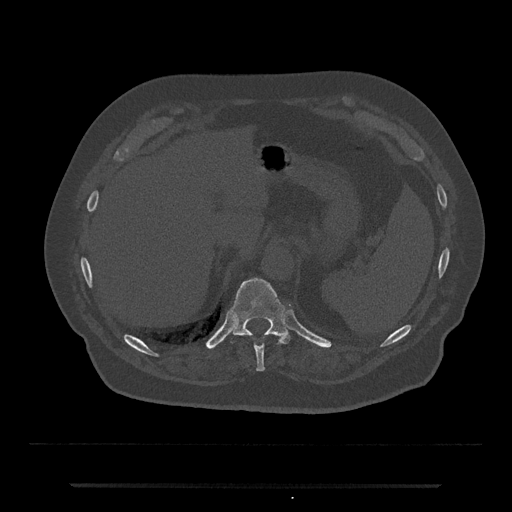
CT including the spine, one axial slice; slice 669 of 797 in the series (ordered by position); reconstruction kernel Br40s/3; 120 kVp; bone window (W 1800 / L 400 HU); 512 × 512 image matrix, field of view 434 × 434 mm. Patient: male, 80 years. Case-level facts recorded for this patient, not image findings: primary cancer: prostate; vertebrae with lytic lesions (as recorded): L1, T11.
Outlined on this slice (semi-automatically segmented with operator editing):
- T10 vertebra: bounding box [x1, y1, x2, y2] px = [254, 345, 265, 371]
- T11 vertebra: [230, 278, 293, 344]